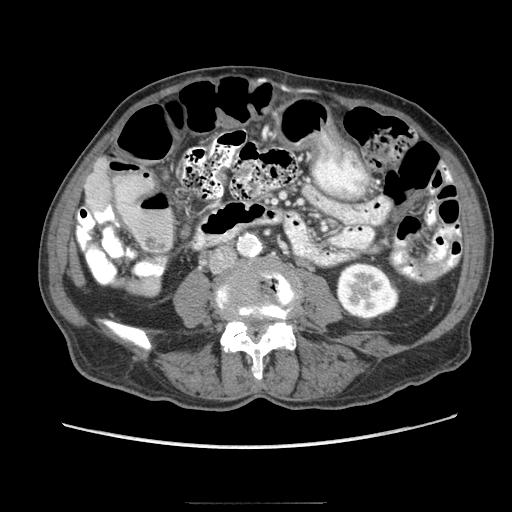
Contrast-enhanced abdominal CT (liver protocol), one axial slice; slice 9 of 83 in the series (ordered by position); reconstruction kernel STANDARD; 140 kVp; soft-tissue window (W 400 / L 40 HU); 512 × 512 image matrix, field of view 360 × 360 mm. From the clinical record (not read from this slice): diagnosis: hepatocellular carcinoma (patient treated with transarterial chemoembolisation; whether this scan precedes or follows treatment is not stated here); TNM stage (as recorded): Stage-I; Child-Pugh class: A; tumour differentiation: moderately differentiated; tumour nodularity: uninodular.
Outlined on this slice (semi-automatic segmentation, software-assisted and operator-edited):
- liver parenchyma outside the tumour (the mass and vessels are separate outlines, so this box may not span the whole liver): bounding box <84,156,110,214> (left, top, right, bottom; pixels)
- liver vessels: <89,201,92,203>